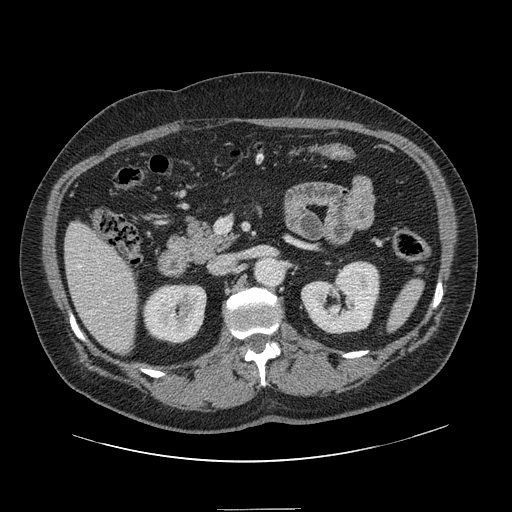
Contrast-enhanced abdominal CT, one axial slice; position 58 of 154 along the scan axis; 120 kVp; intravenous contrast given; soft-tissue window (W 400 / L 40 HU); 2.5 mm slice thickness; 512 × 512 image matrix, field of view 451 × 451 mm. Male patient, age 61 years. From the clinical record (not read from this slice): diagnosis: colorectal cancer liver metastases, imaged before liver resection.
Outlined on this slice (expert manual segmentation):
- hepatic veins: bounding box (x1, y1, x2, y2) in pixels: (78, 265, 106, 305)
- liver: (66, 223, 138, 353)
- planned liver remnant (the part of the liver to remain after resection): (66, 223, 138, 354)